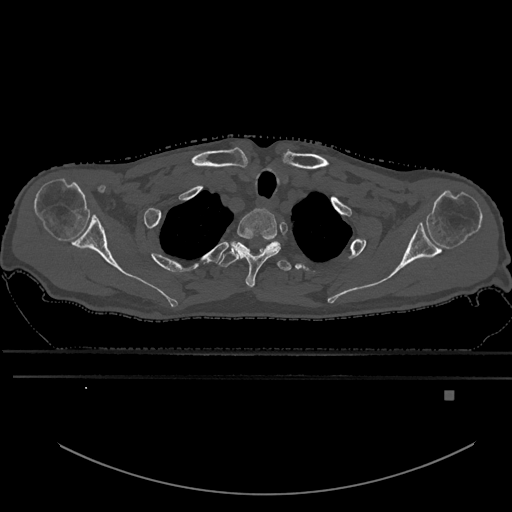
CT including the spine, one axial slice; slice 521 of 969 in the series (ordered by position); bone window (W 1800 / L 400 HU); 0.5 mm slice thickness; 512 × 512 image matrix. Male patient, age 82 years. From the clinical record (not read from this slice): primary cancer: prostate; vertebrae with lytic lesions (as recorded): T11, T9, T8, T2.
Annotated regions visible in this slice (semi-automatically segmented with operator editing):
- T1 vertebra: bounding box <236,208,281,288> (left, top, right, bottom; pixels)
- T2 vertebra: <218,238,280,267>